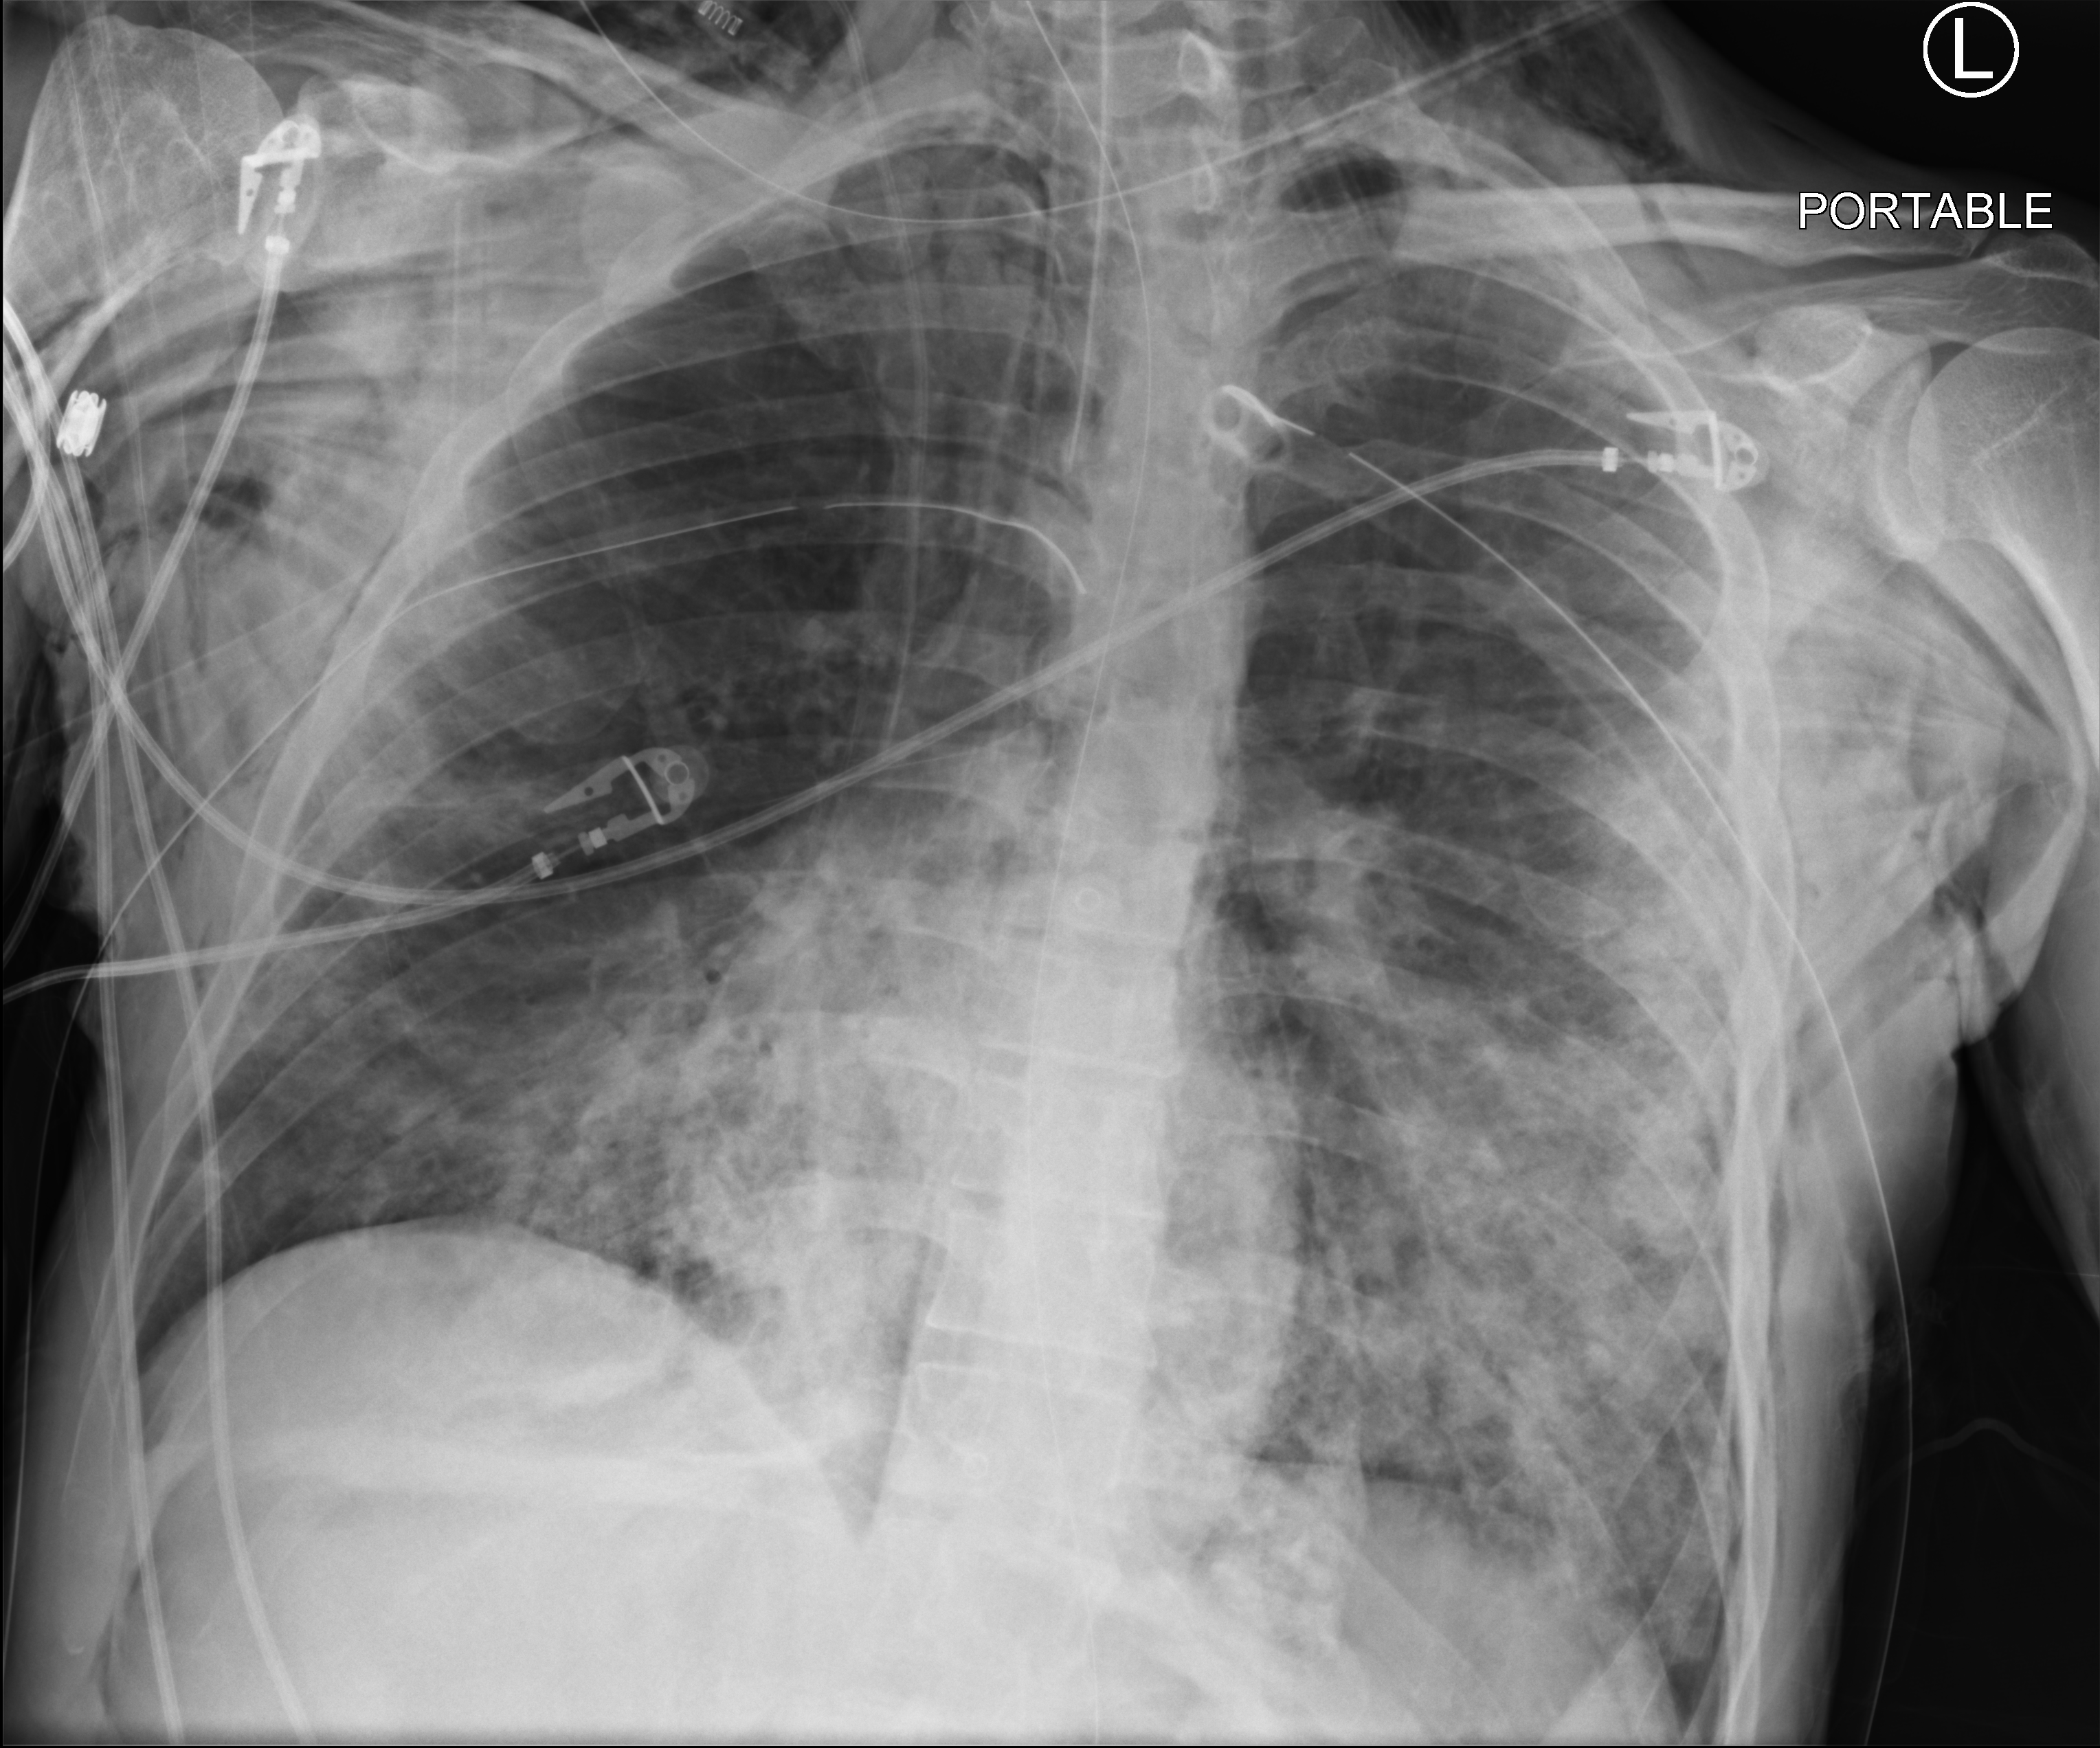
Portable chest radiograph; anteroposterior (AP) projection. Patient hospitalised with COVID-19; male, aged 18–59 years.
From the hospital-stay record, not from the radiograph (when in the stay this image was taken is not recorded): mechanically ventilated during this hospital stay: yes; admitted to intensive care during this hospital stay: yes.